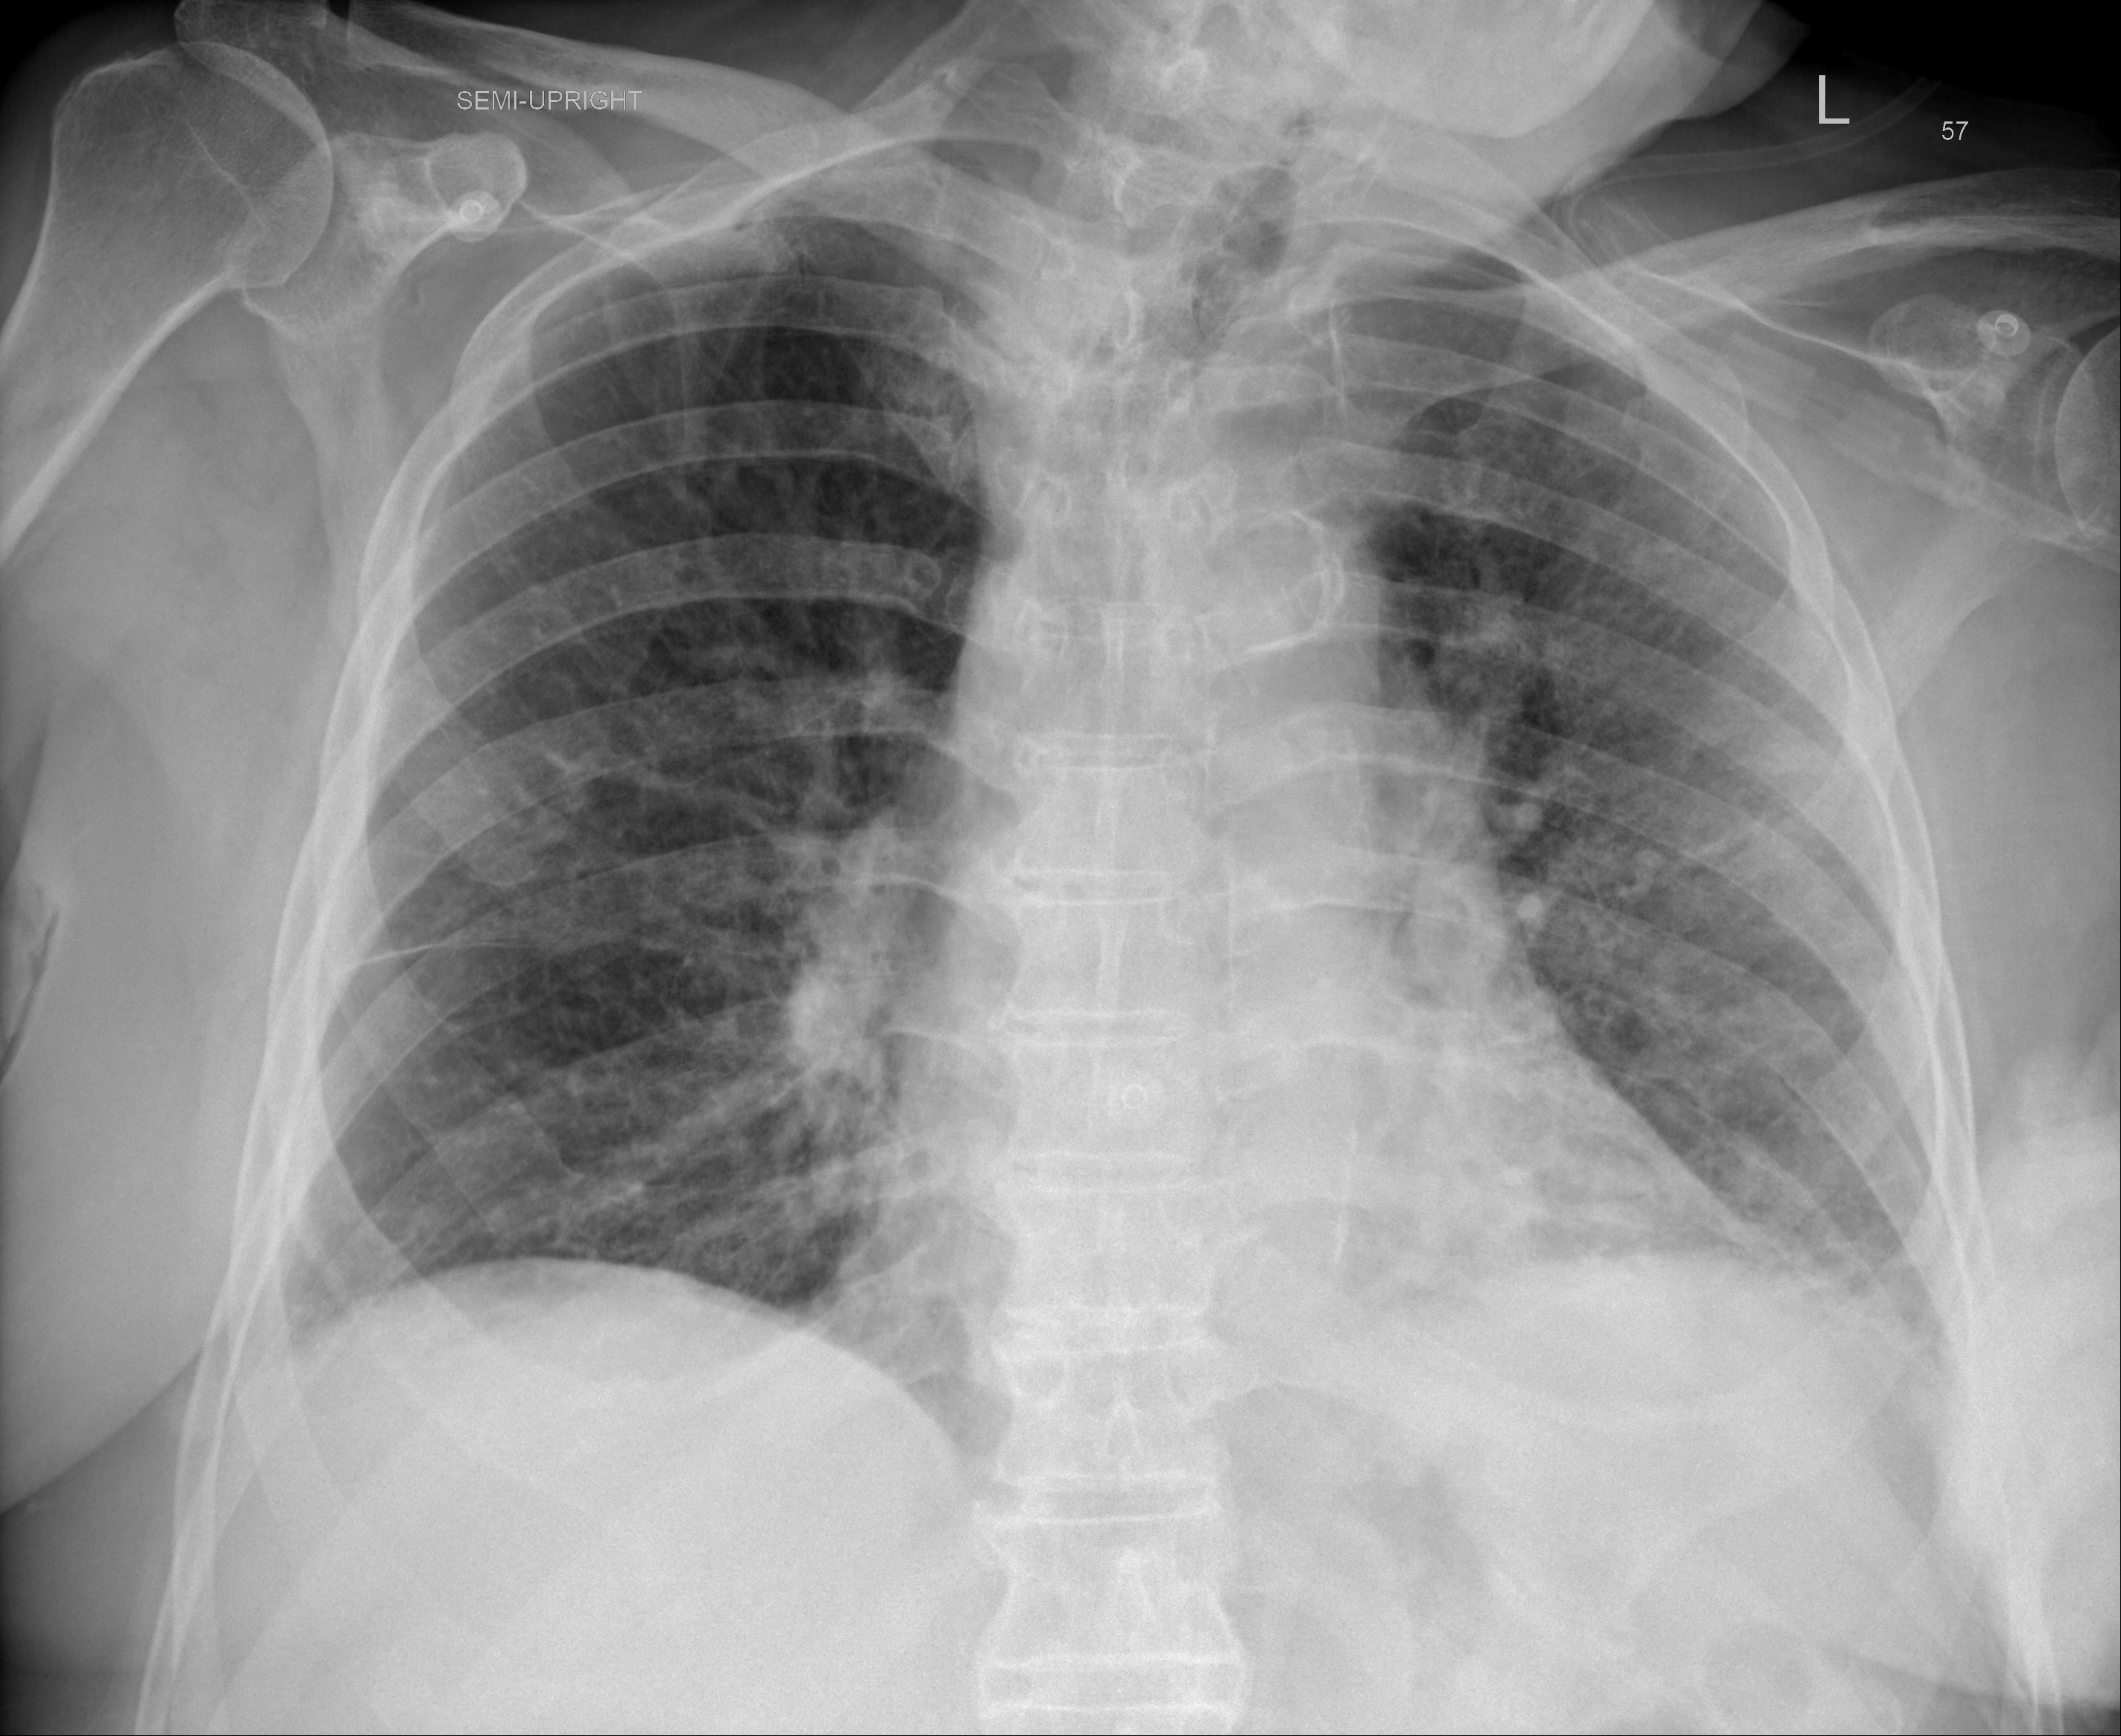
Chest X-ray (portable), AP projection. Male patient, age 89 years; imaged 5 days after the COVID-19 diagnosis.
Radiologist's key findings for this exam: Persistent minimally improved airspace disease within the left mid and lower lung.